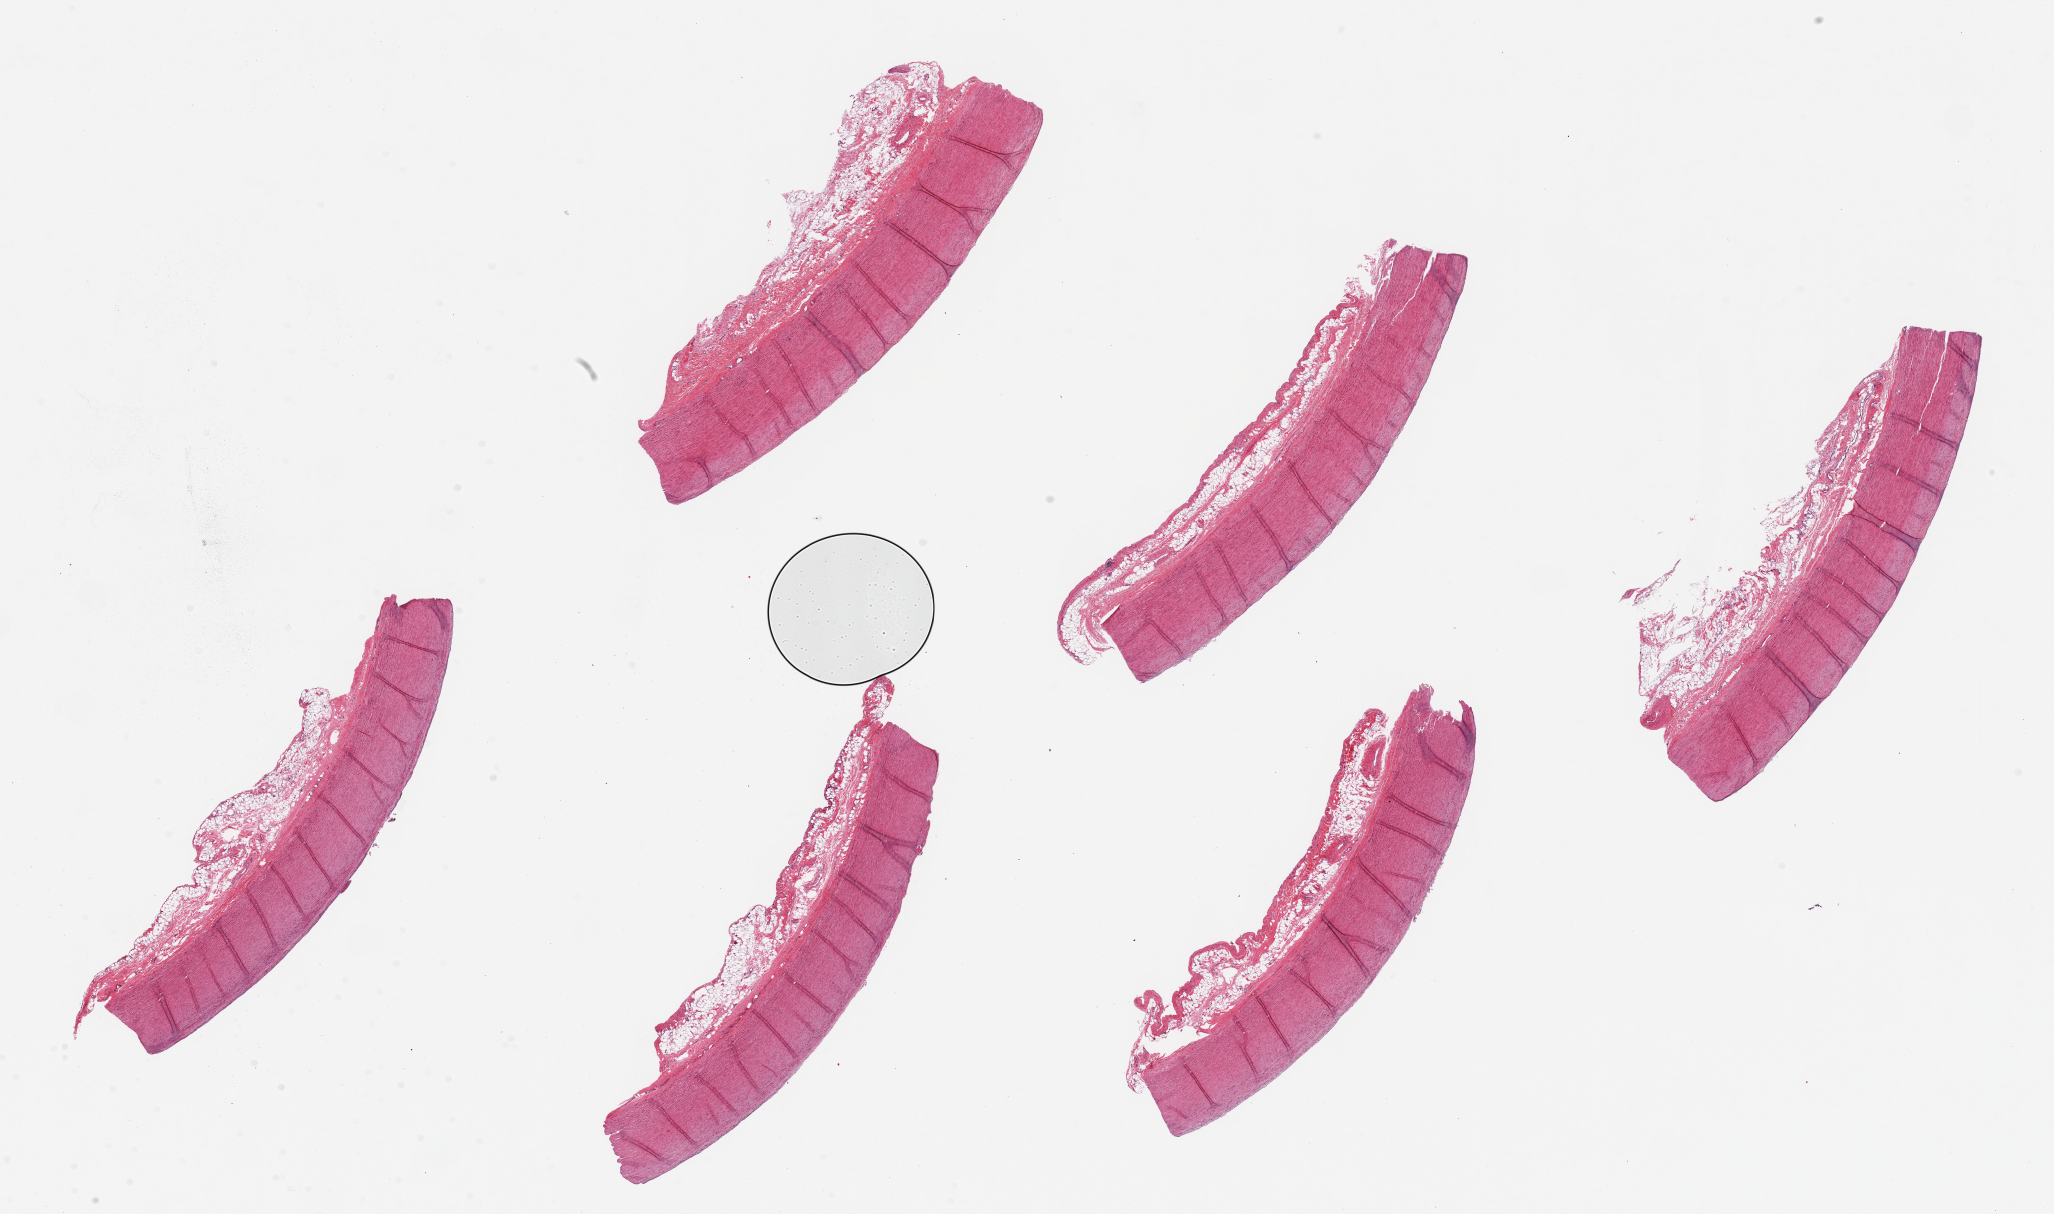
Whole-slide image, hematoxylin and eosin (H&E) stain, brightfield, whole scanned area (about 32.5 x 19.2 mm) shown as a low-resolution overview; PAXgene-fixed, paraffin-embedded tissue; sampled site (target tissue): aorta; donor tissue sample. Donor: male.
Review note (as recorded): 6 pieces ~8x2mm, ~25% thickness is adventitial fat/vasa vasorum.